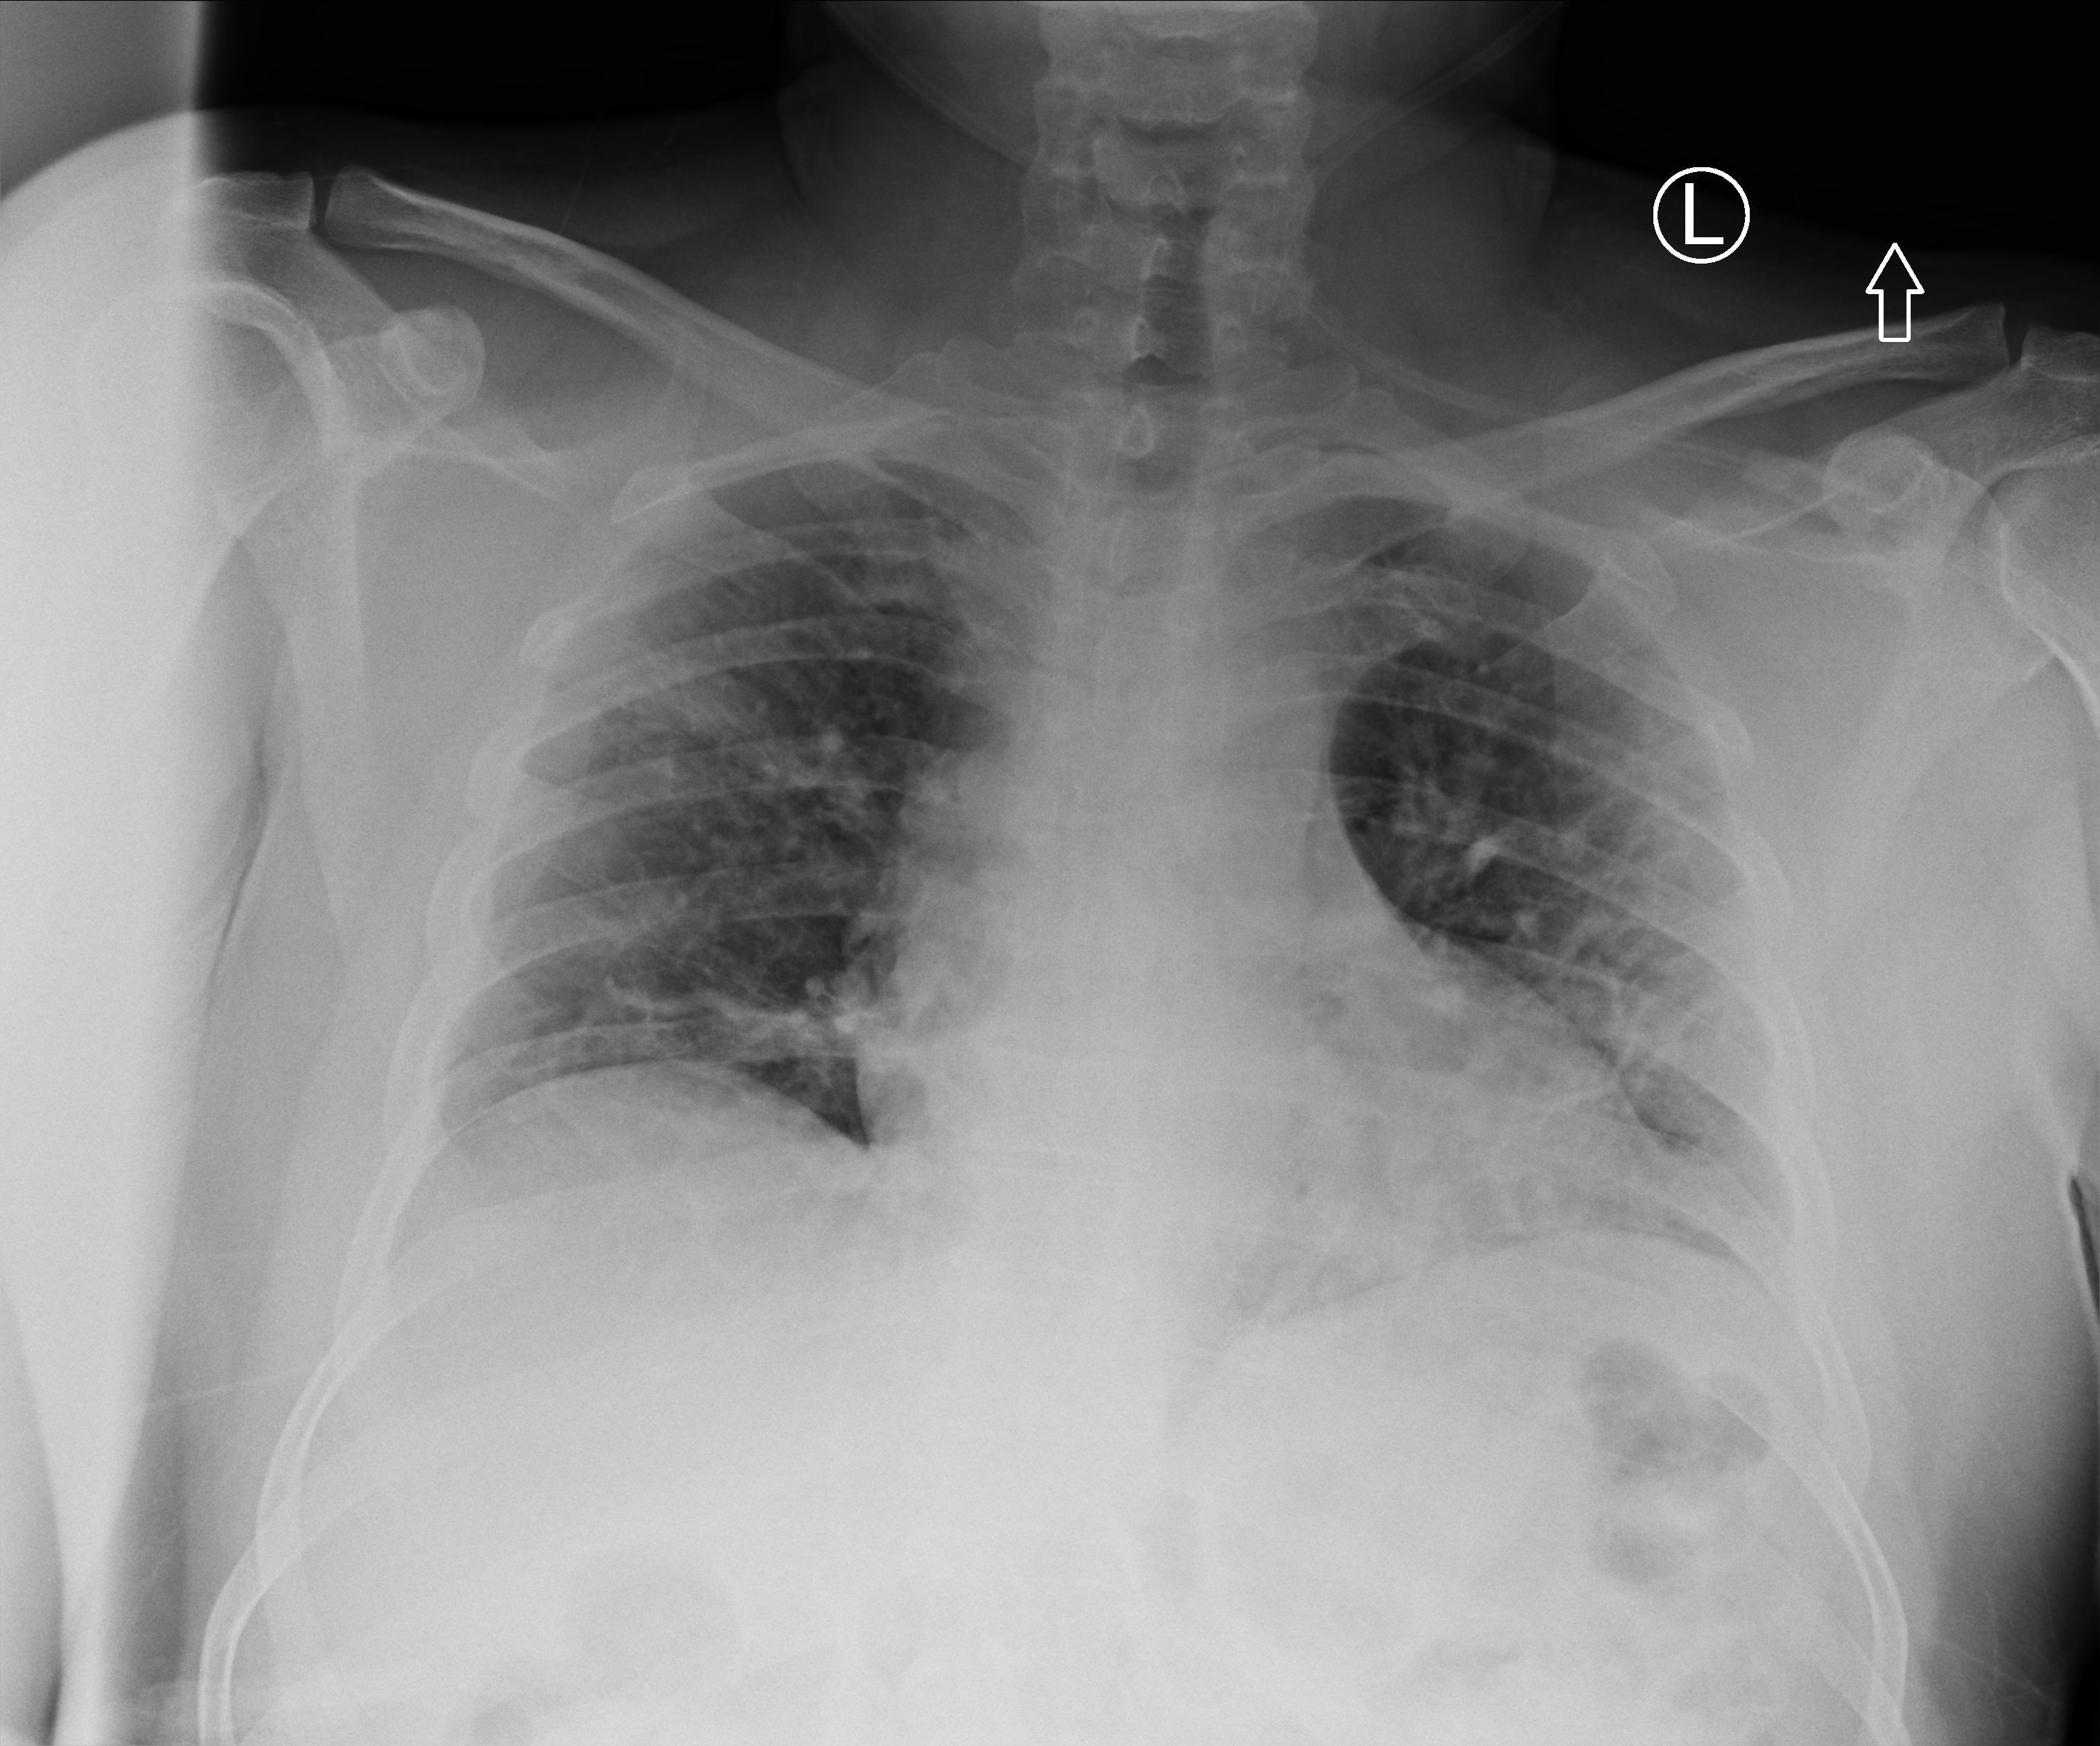
Bedside chest radiograph (computed radiography); anteroposterior (AP) projection. Male patient hospitalised with COVID-19, age 18–59 years.
Admission-level facts for this patient (not findings on this image; timing relative to this image not recorded):
- admitted to intensive care during this hospital stay: no
- other chronic lung disease (admission record): no